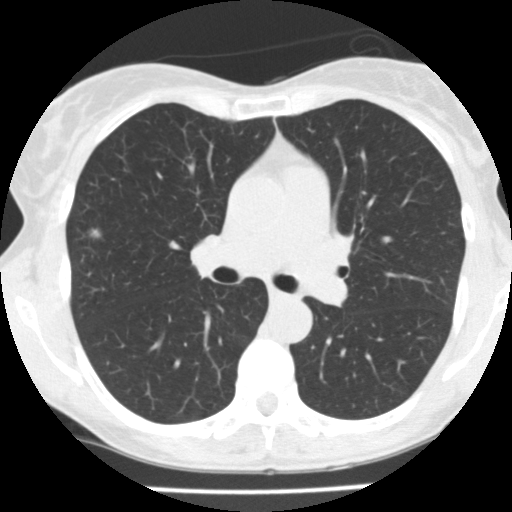
Low-dose screening chest CT, one axial slice. Slice 103 of 166 in the series (ordered by position). Lung window (W 1500 / L -600 HU). 512 × 512 image matrix.
Annotated regions visible in this slice (expert manual segmentation):
- lesion 1 (tumor, upper lobe of right lung): box from (x=91, y=230) to (x=100, y=237) px